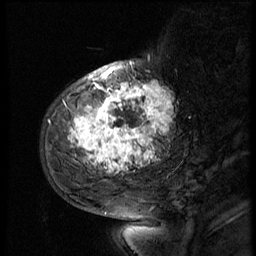
Breast MRI (dynamic contrast-enhanced), one sagittal slice; slice 17 of 56 in the series (ordered by position); 3 images stored at this slice position (order not interpretable as contrast timing); 1.5 T; TE 4.2 ms, TR 9 ms; 2.5 mm slice thickness; 256 × 256 image matrix, field of view 180 × 180 mm. Female patient, age 51 years. Case-level facts recorded for this patient, not image findings: setting: breast cancer imaged before/during neoadjuvant chemotherapy; receptor status: triple-negative.
Annotated regions visible in this slice (semi-automatically segmented with operator editing):
- analysis volume of interest (the breast-tissue region the enhancement analysis was run in; not a lesion): bounding box <52,66,183,179> (left, top, right, bottom; pixels)
- tumour enhancement mask (voxels above the 140 % enhancement threshold inside the analysis volume of interest): <68,68,172,173>